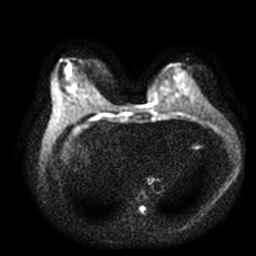
Breast MRI, one axial slice; slice 13 of 40 in the series (ordered by position); diffusion-weighted series; image 2 of 4 stored at this slice position (different b-values; order by instance number); 3 T; 5 mm slice thickness; 256 × 256 image matrix, field of view 360 × 360 mm. Female patient.
Annotated regions visible in this slice (outlined manually by an expert reader):
- tumour on diffusion-weighted imaging: bounding box <67,66,71,74> (left, top, right, bottom; pixels)